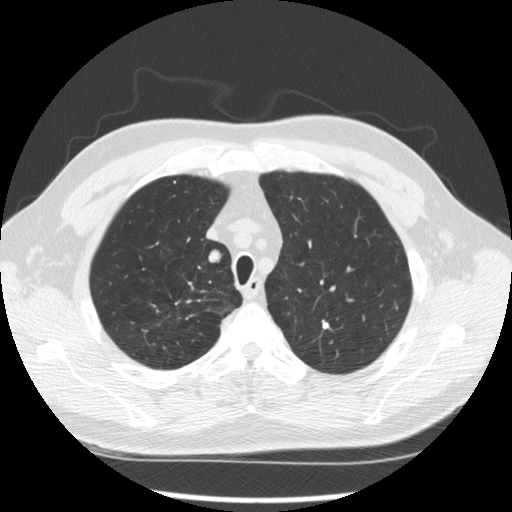
Chest CT (low-dose screening protocol), one axial image; second screening round (one year after baseline); lung window (W 1500 / L -600 HU); 2.5 mm slice thickness; standard (soft-tissue) reconstruction kernel (STANDARD); slice 54 of 289 in the series. Male participant, aged 64 years at enrolment.
• Expert reader's lesion annotation, bounding box <193,245,226,274> (left, top, right, bottom; pixels).
• The screening reader recorded 3 non-calcified nodules or masses ≥4 mm on this exam; which of them this box marks is not recorded.
• Participant outcome: lung cancer diagnosed 411 days after this screen (after the third annual screen) — adenocarcinoma, NOS, right upper lobe, moderately differentiated (G2), stage IA (AJCC 6th edition), 14 mm at pathology.